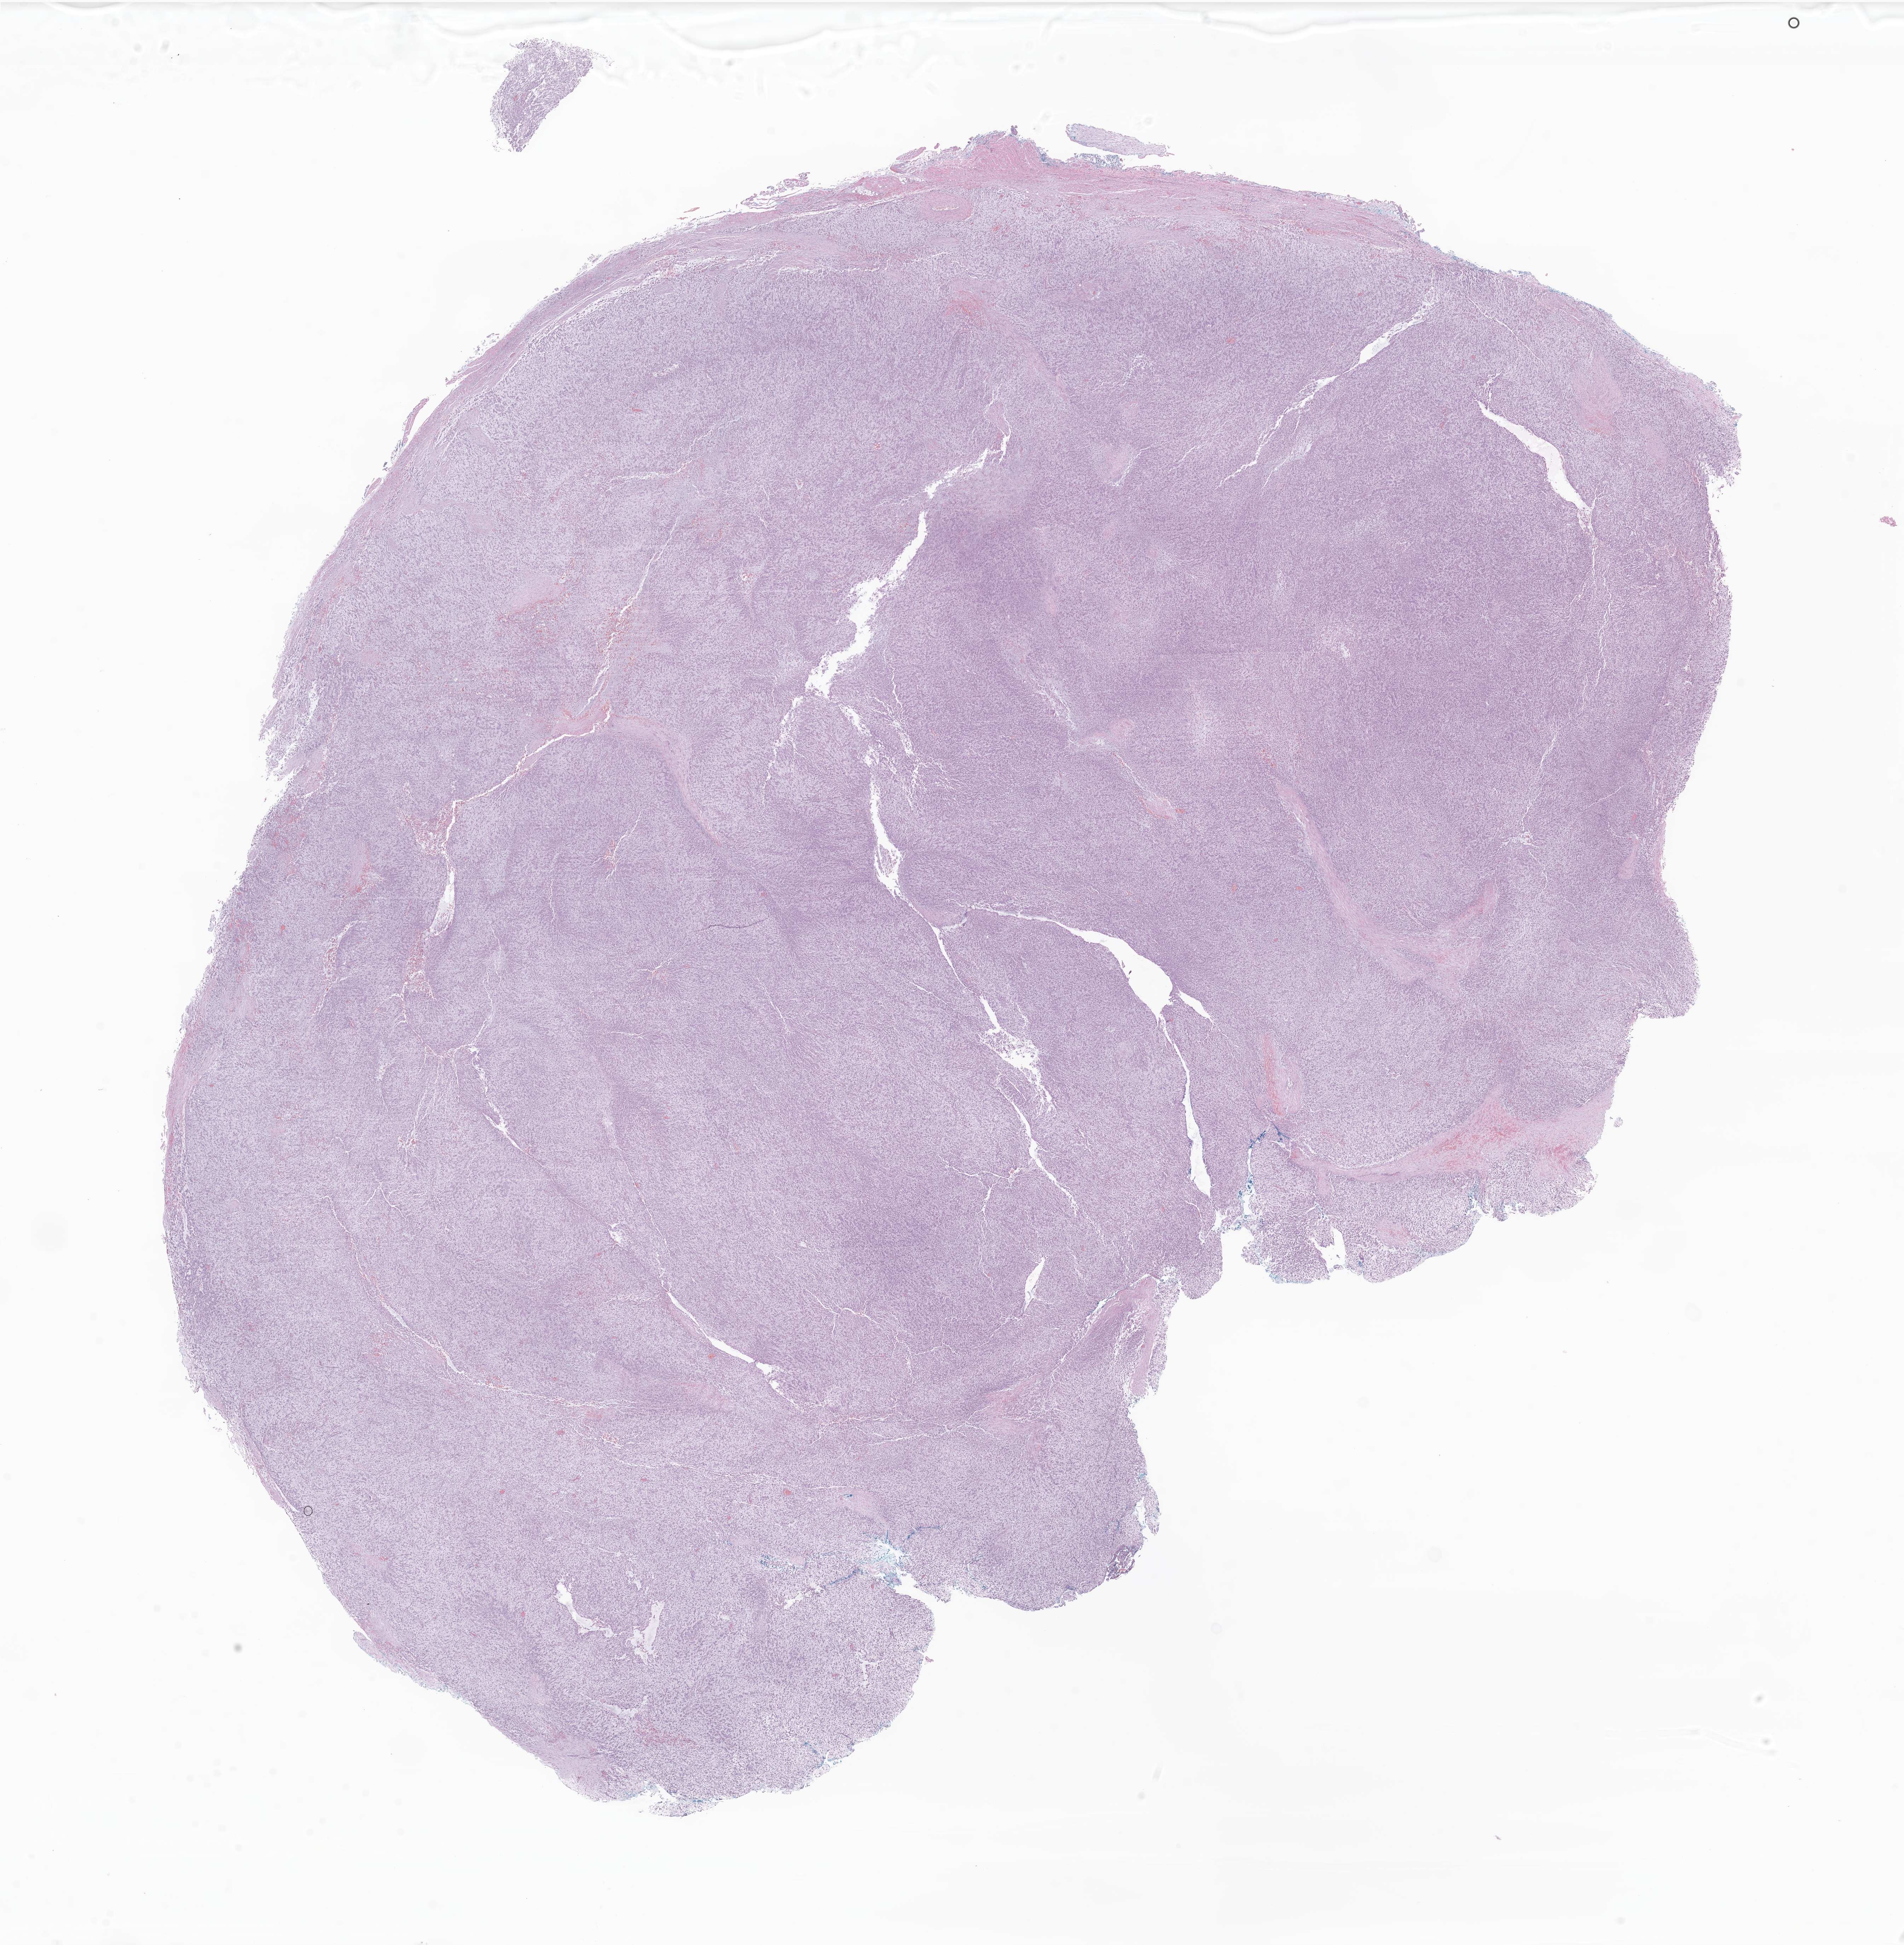
H&E whole-slide image of tumor tissue from the orbit, a low-resolution overview of the entire scanned area, about 22.7 x 23.2 mm; formalin-fixed paraffin-embedded section. Female patient, age 88 days.
* diagnosis: Undifferentiated sarcoma